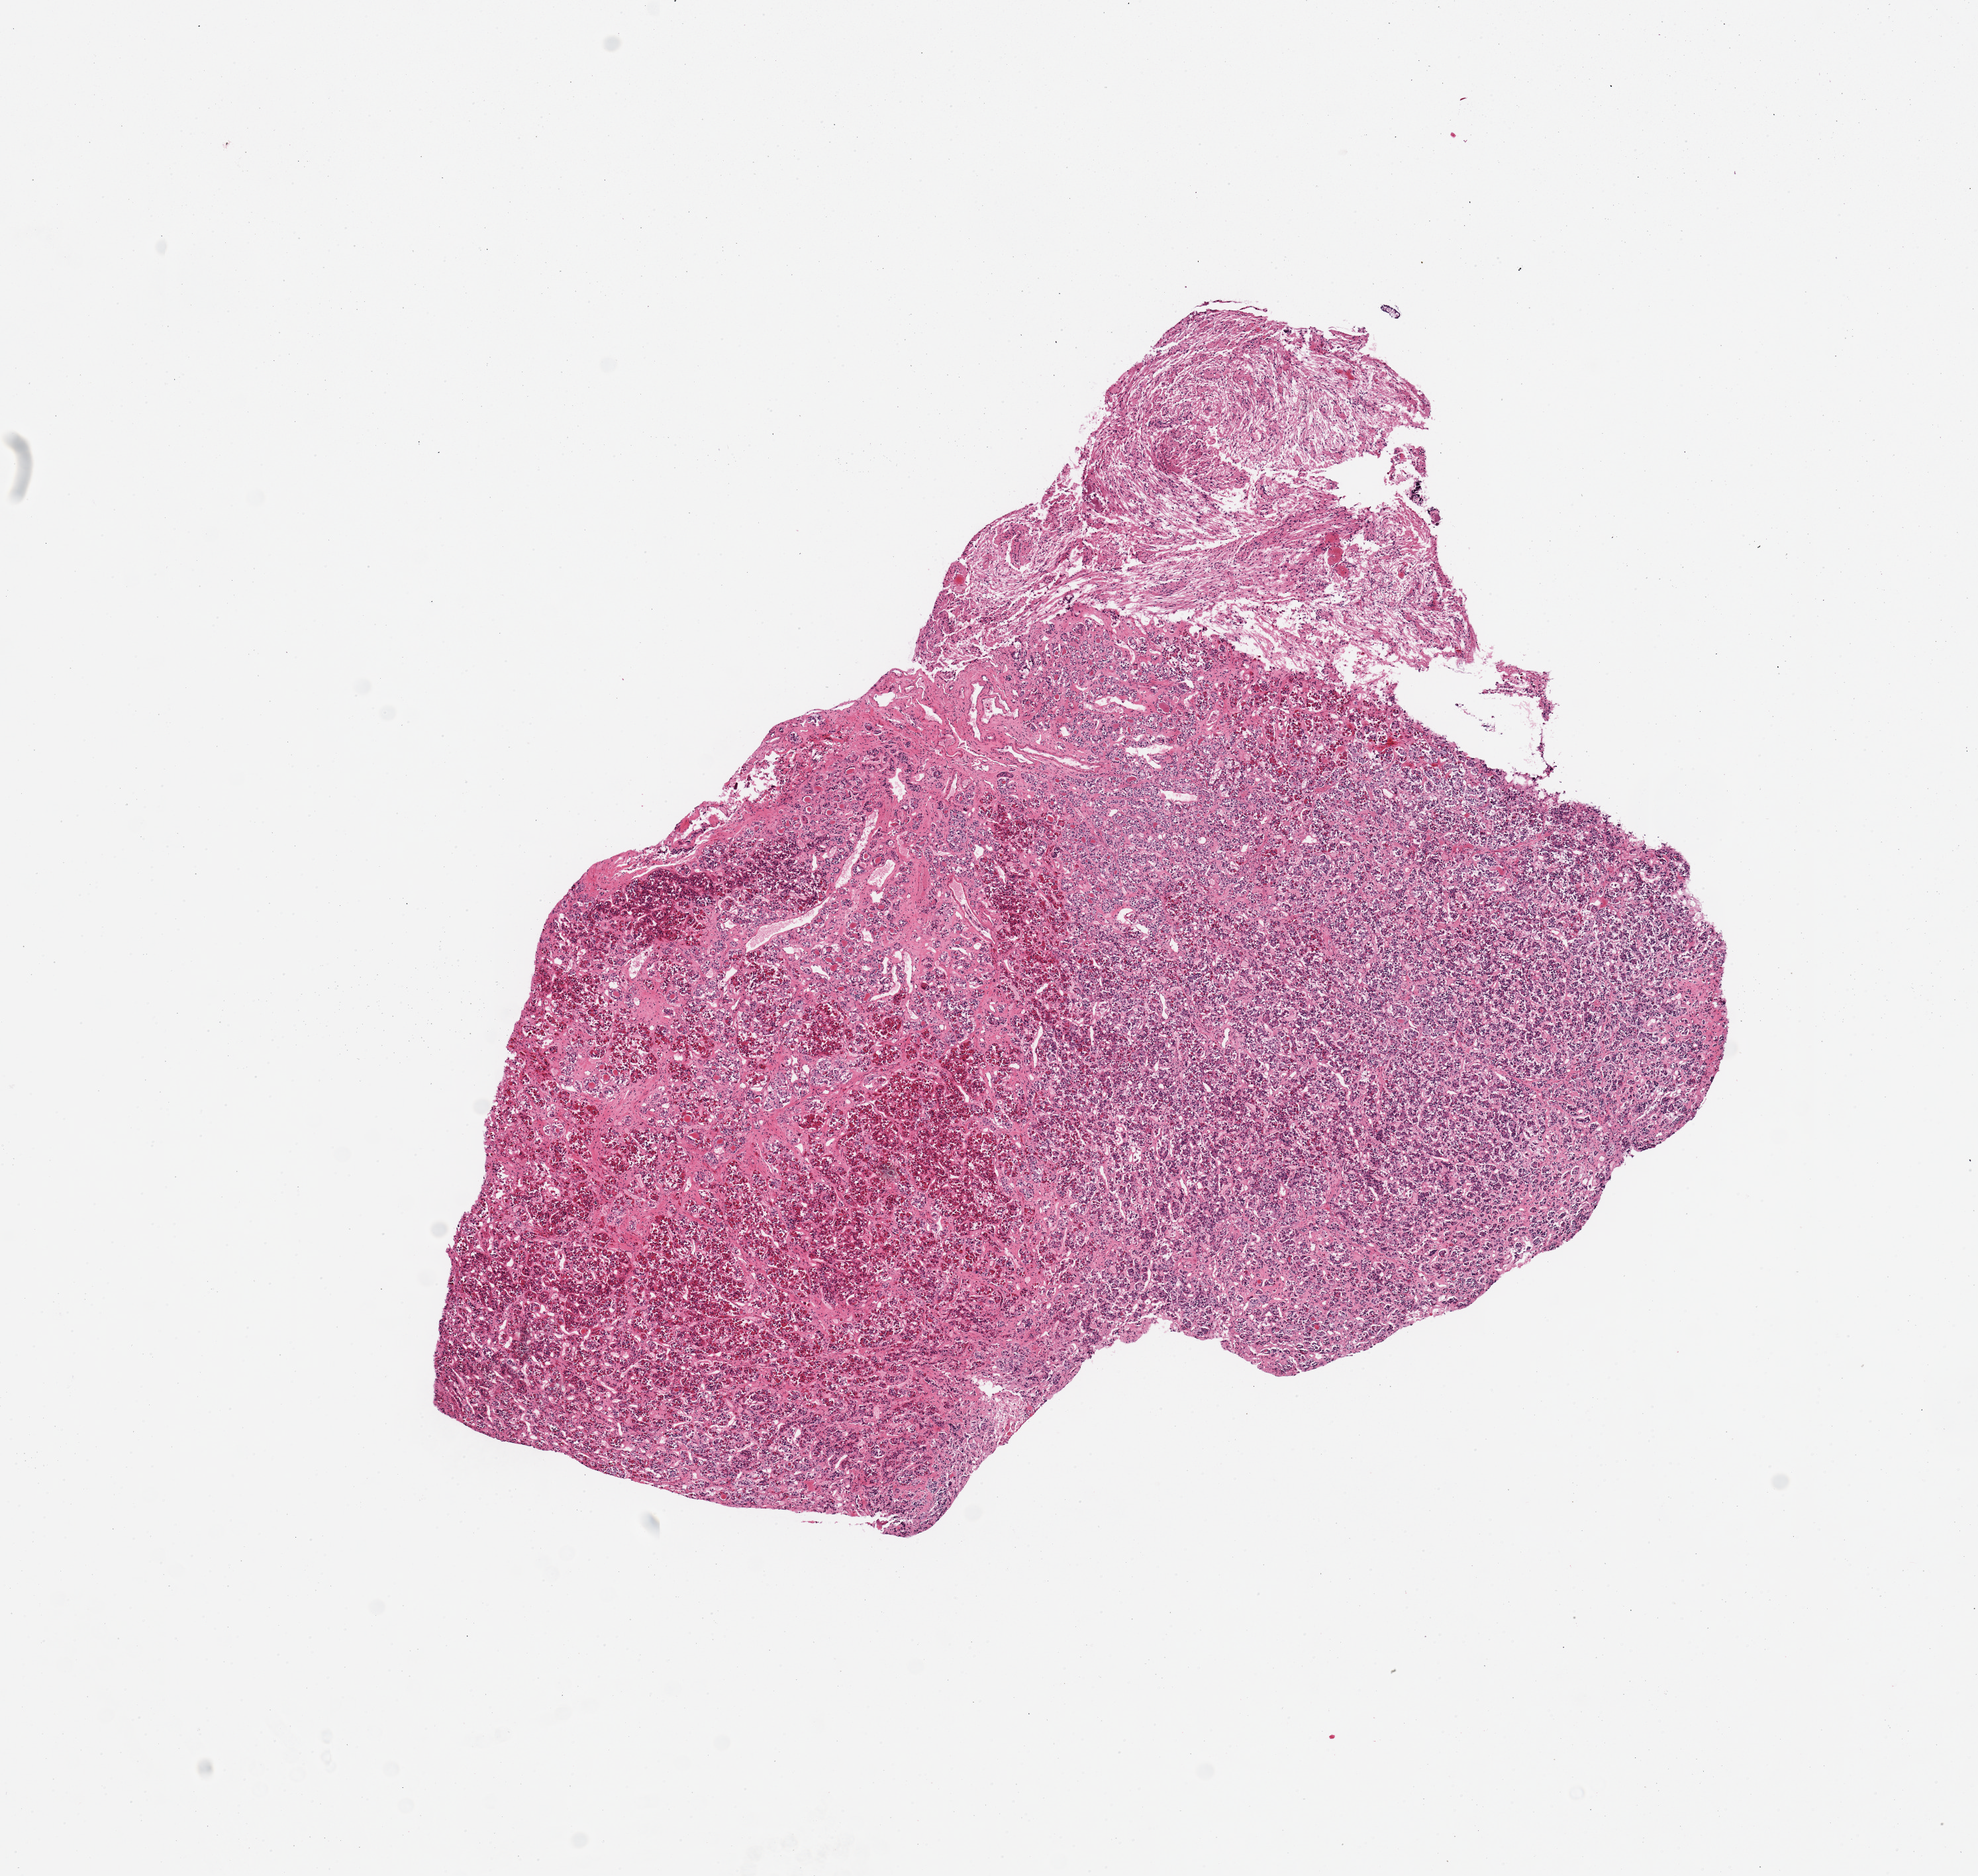
Whole-slide image, hematoxylin and eosin (H&E) stain — low-resolution overview of the scanned area, about 11.8 x 11.2 mm; PAXgene-fixed, paraffin-embedded tissue; sampled site (target tissue): pituitary; tissue donor sample. Donor sex: male.
- reviewer comment on this tissue sample: 1 piece; 20% neurohypophysis and 80% adenohypophysis